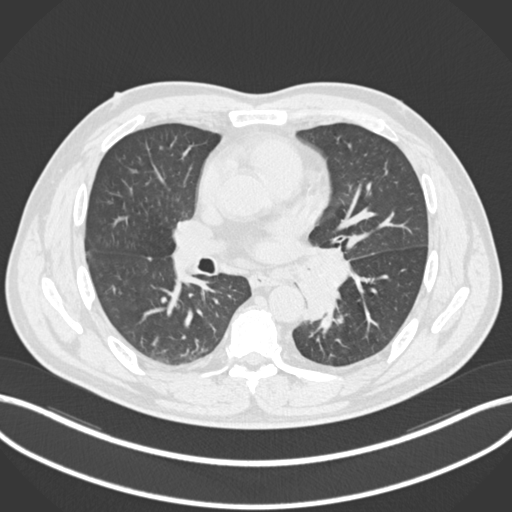
Chest CT, one axial slice. Slice 119 of 223 in the series (ordered by position). Lung window (W 1500 / L -600 HU). 1 mm slice thickness. 512 × 512 image matrix. Male patient, age 50 years. From the clinical record (not read from this slice): clinical TNM (as recorded): T2a N3 M0.
Outlined on this slice (bounding box drawn by a radiologist):
- lung tumour (recorded histology: squamous cell carcinoma): bounding box [x1, y1, x2, y2] px = [294, 241, 349, 323]